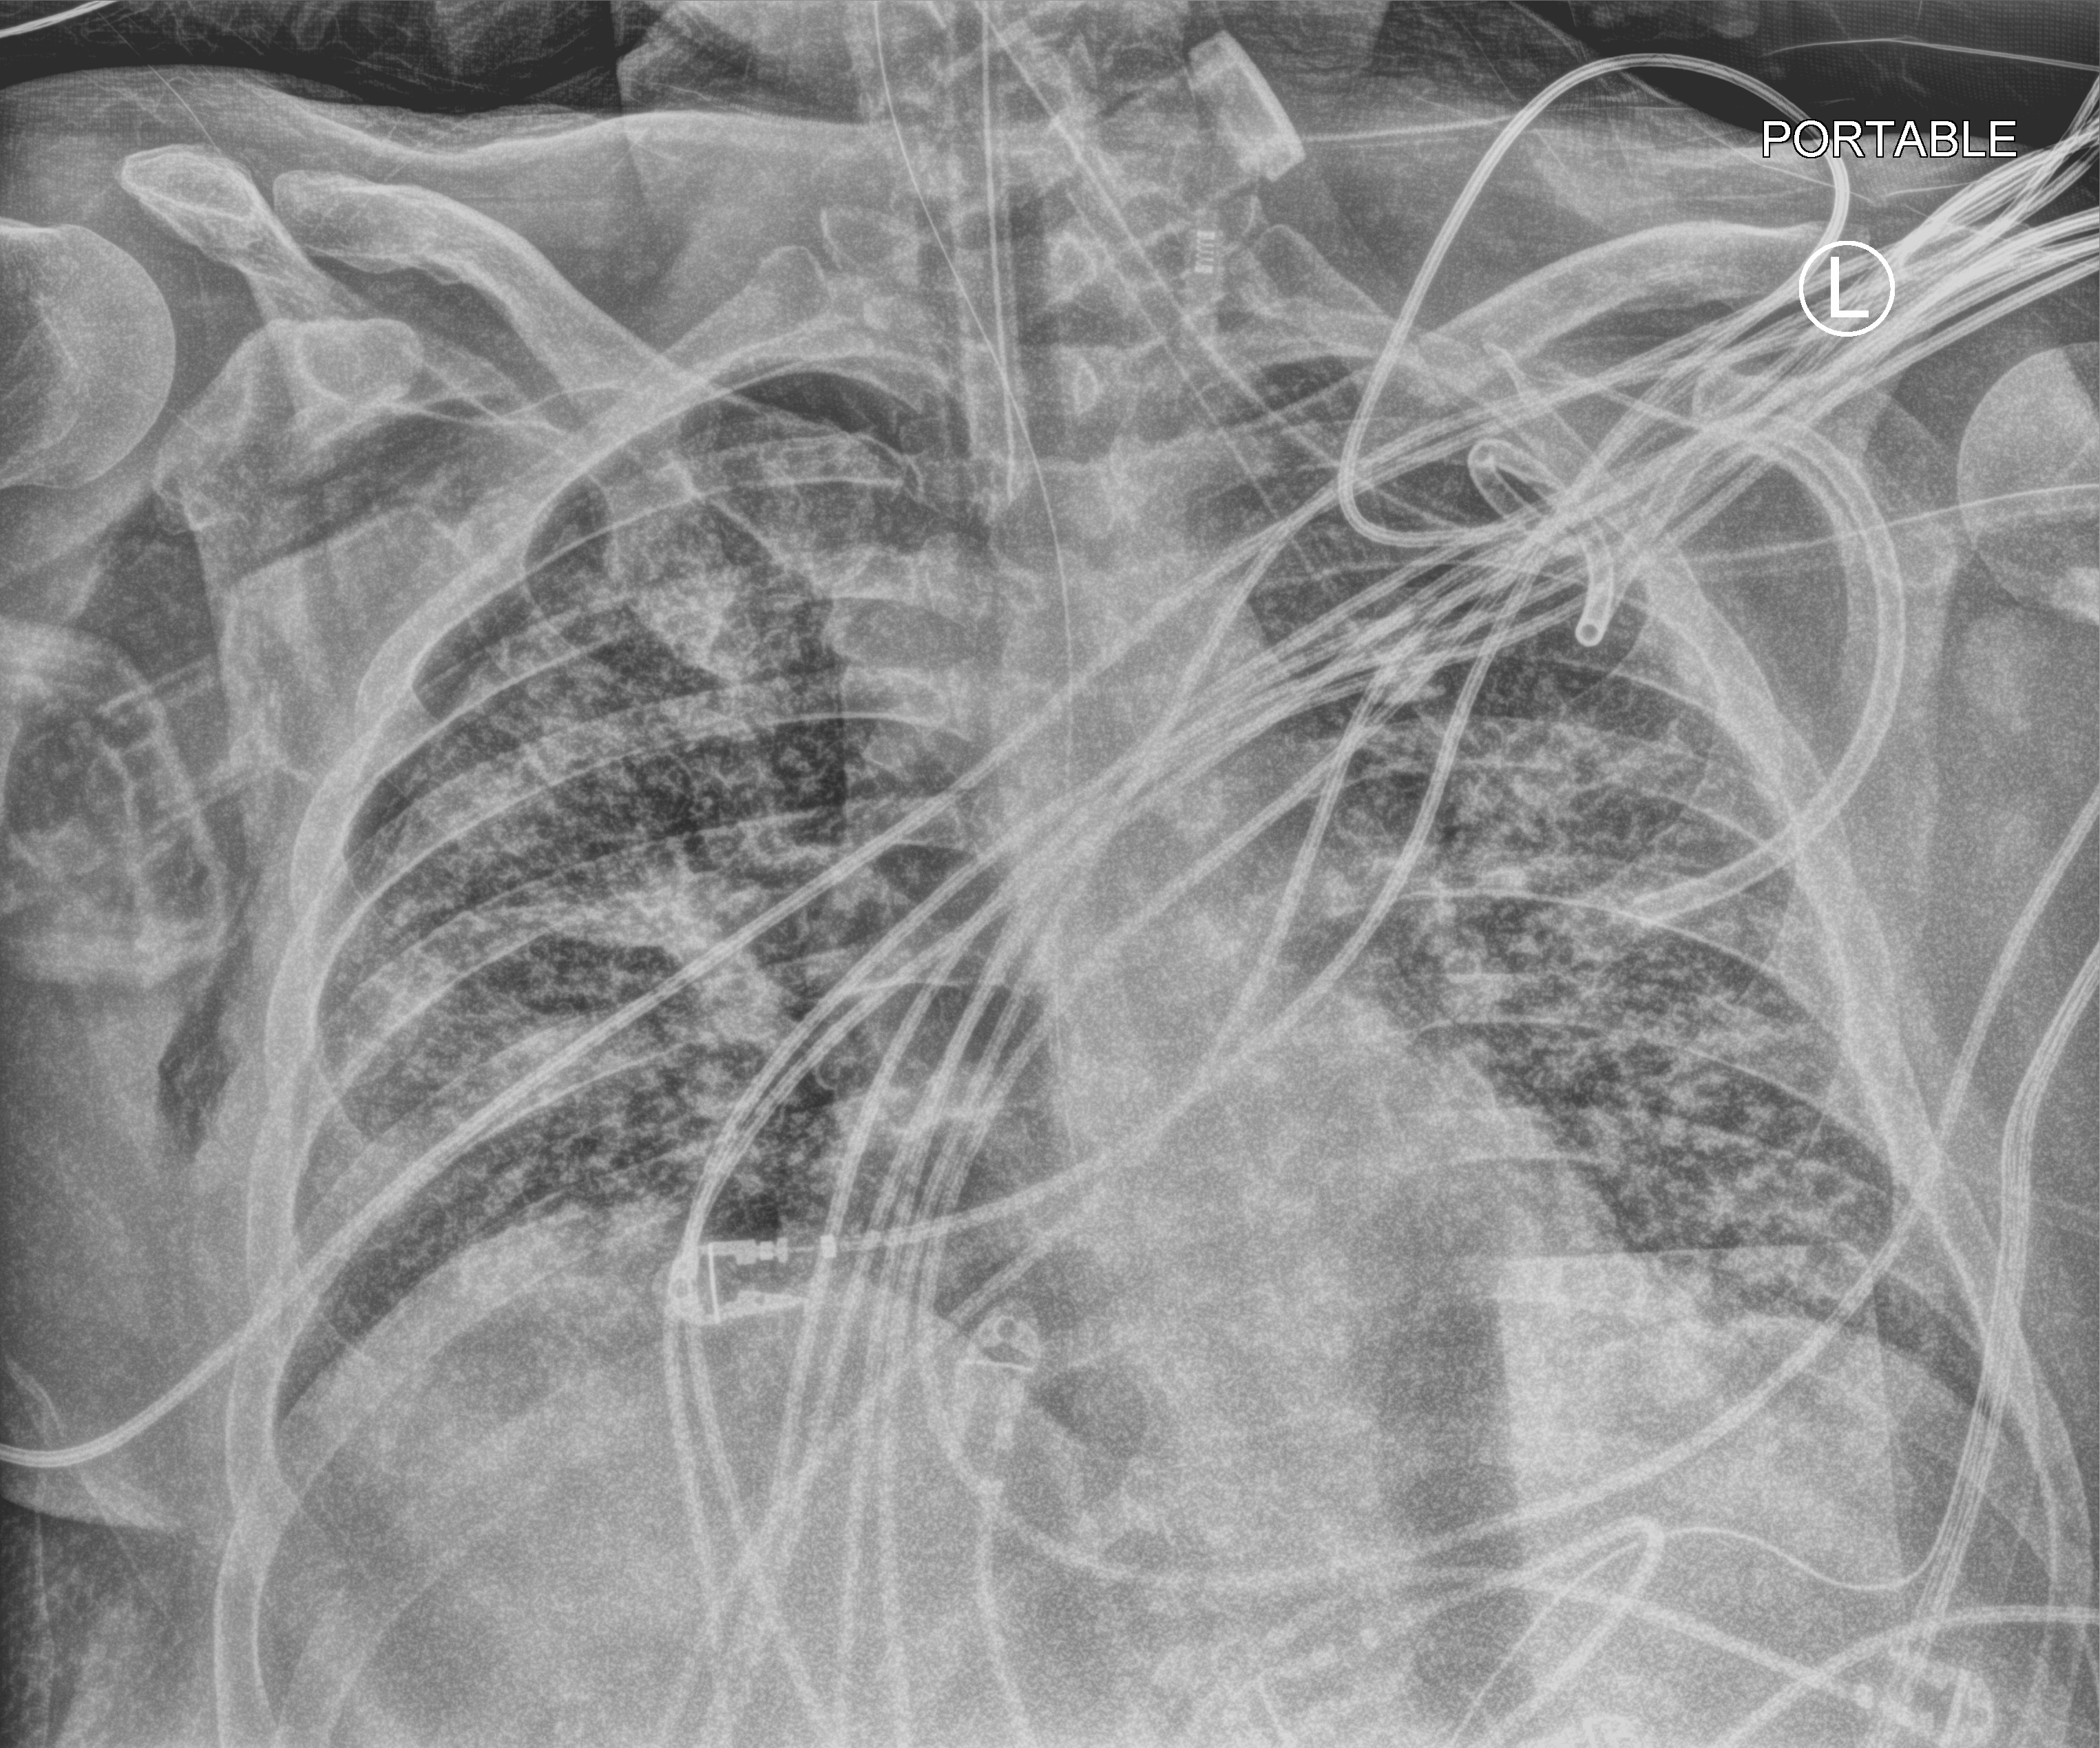
Chest X-ray (portable), anteroposterior (AP) projection. Adult patient hospitalised with COVID-19, age 18–59 years.
From the hospital-stay record, not from the radiograph (when in the stay this image was taken is not recorded):
- mechanically ventilated during this hospital stay: yes
- admitted to intensive care during this hospital stay: yes